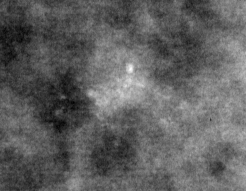
Region of interest cut from a scanned film mammogram (one marked finding); right breast; MLO view; BI-RADS breast density category 3 (scale 1–4).
Finding: calcifications, morphology pleomorphic, distribution clustered; BI-RADS assessment category 4; pathology (as recorded): malignant.